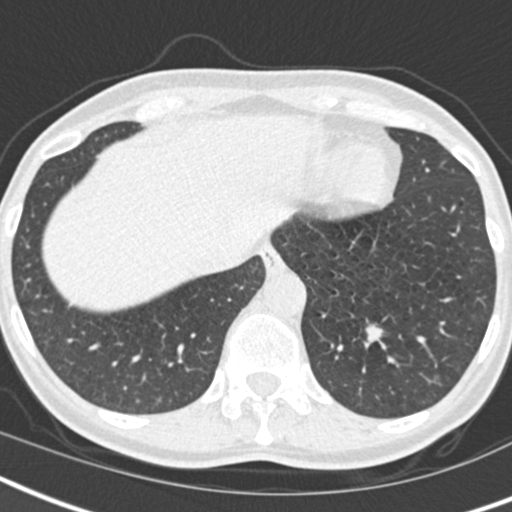
Low-dose screening chest CT, one axial slice; position 46 of 173 along the scan axis; reconstruction kernel B30f; 120 kVp; lung window (W 1500 / L -600 HU); 2 mm slice thickness; 512 × 512 image matrix.
Annotated regions visible in this slice (manually delineated by an expert):
- lesion 1 (tumor, lower lobe of left lung): bounding box [x1, y1, x2, y2] px = [365, 324, 383, 343]